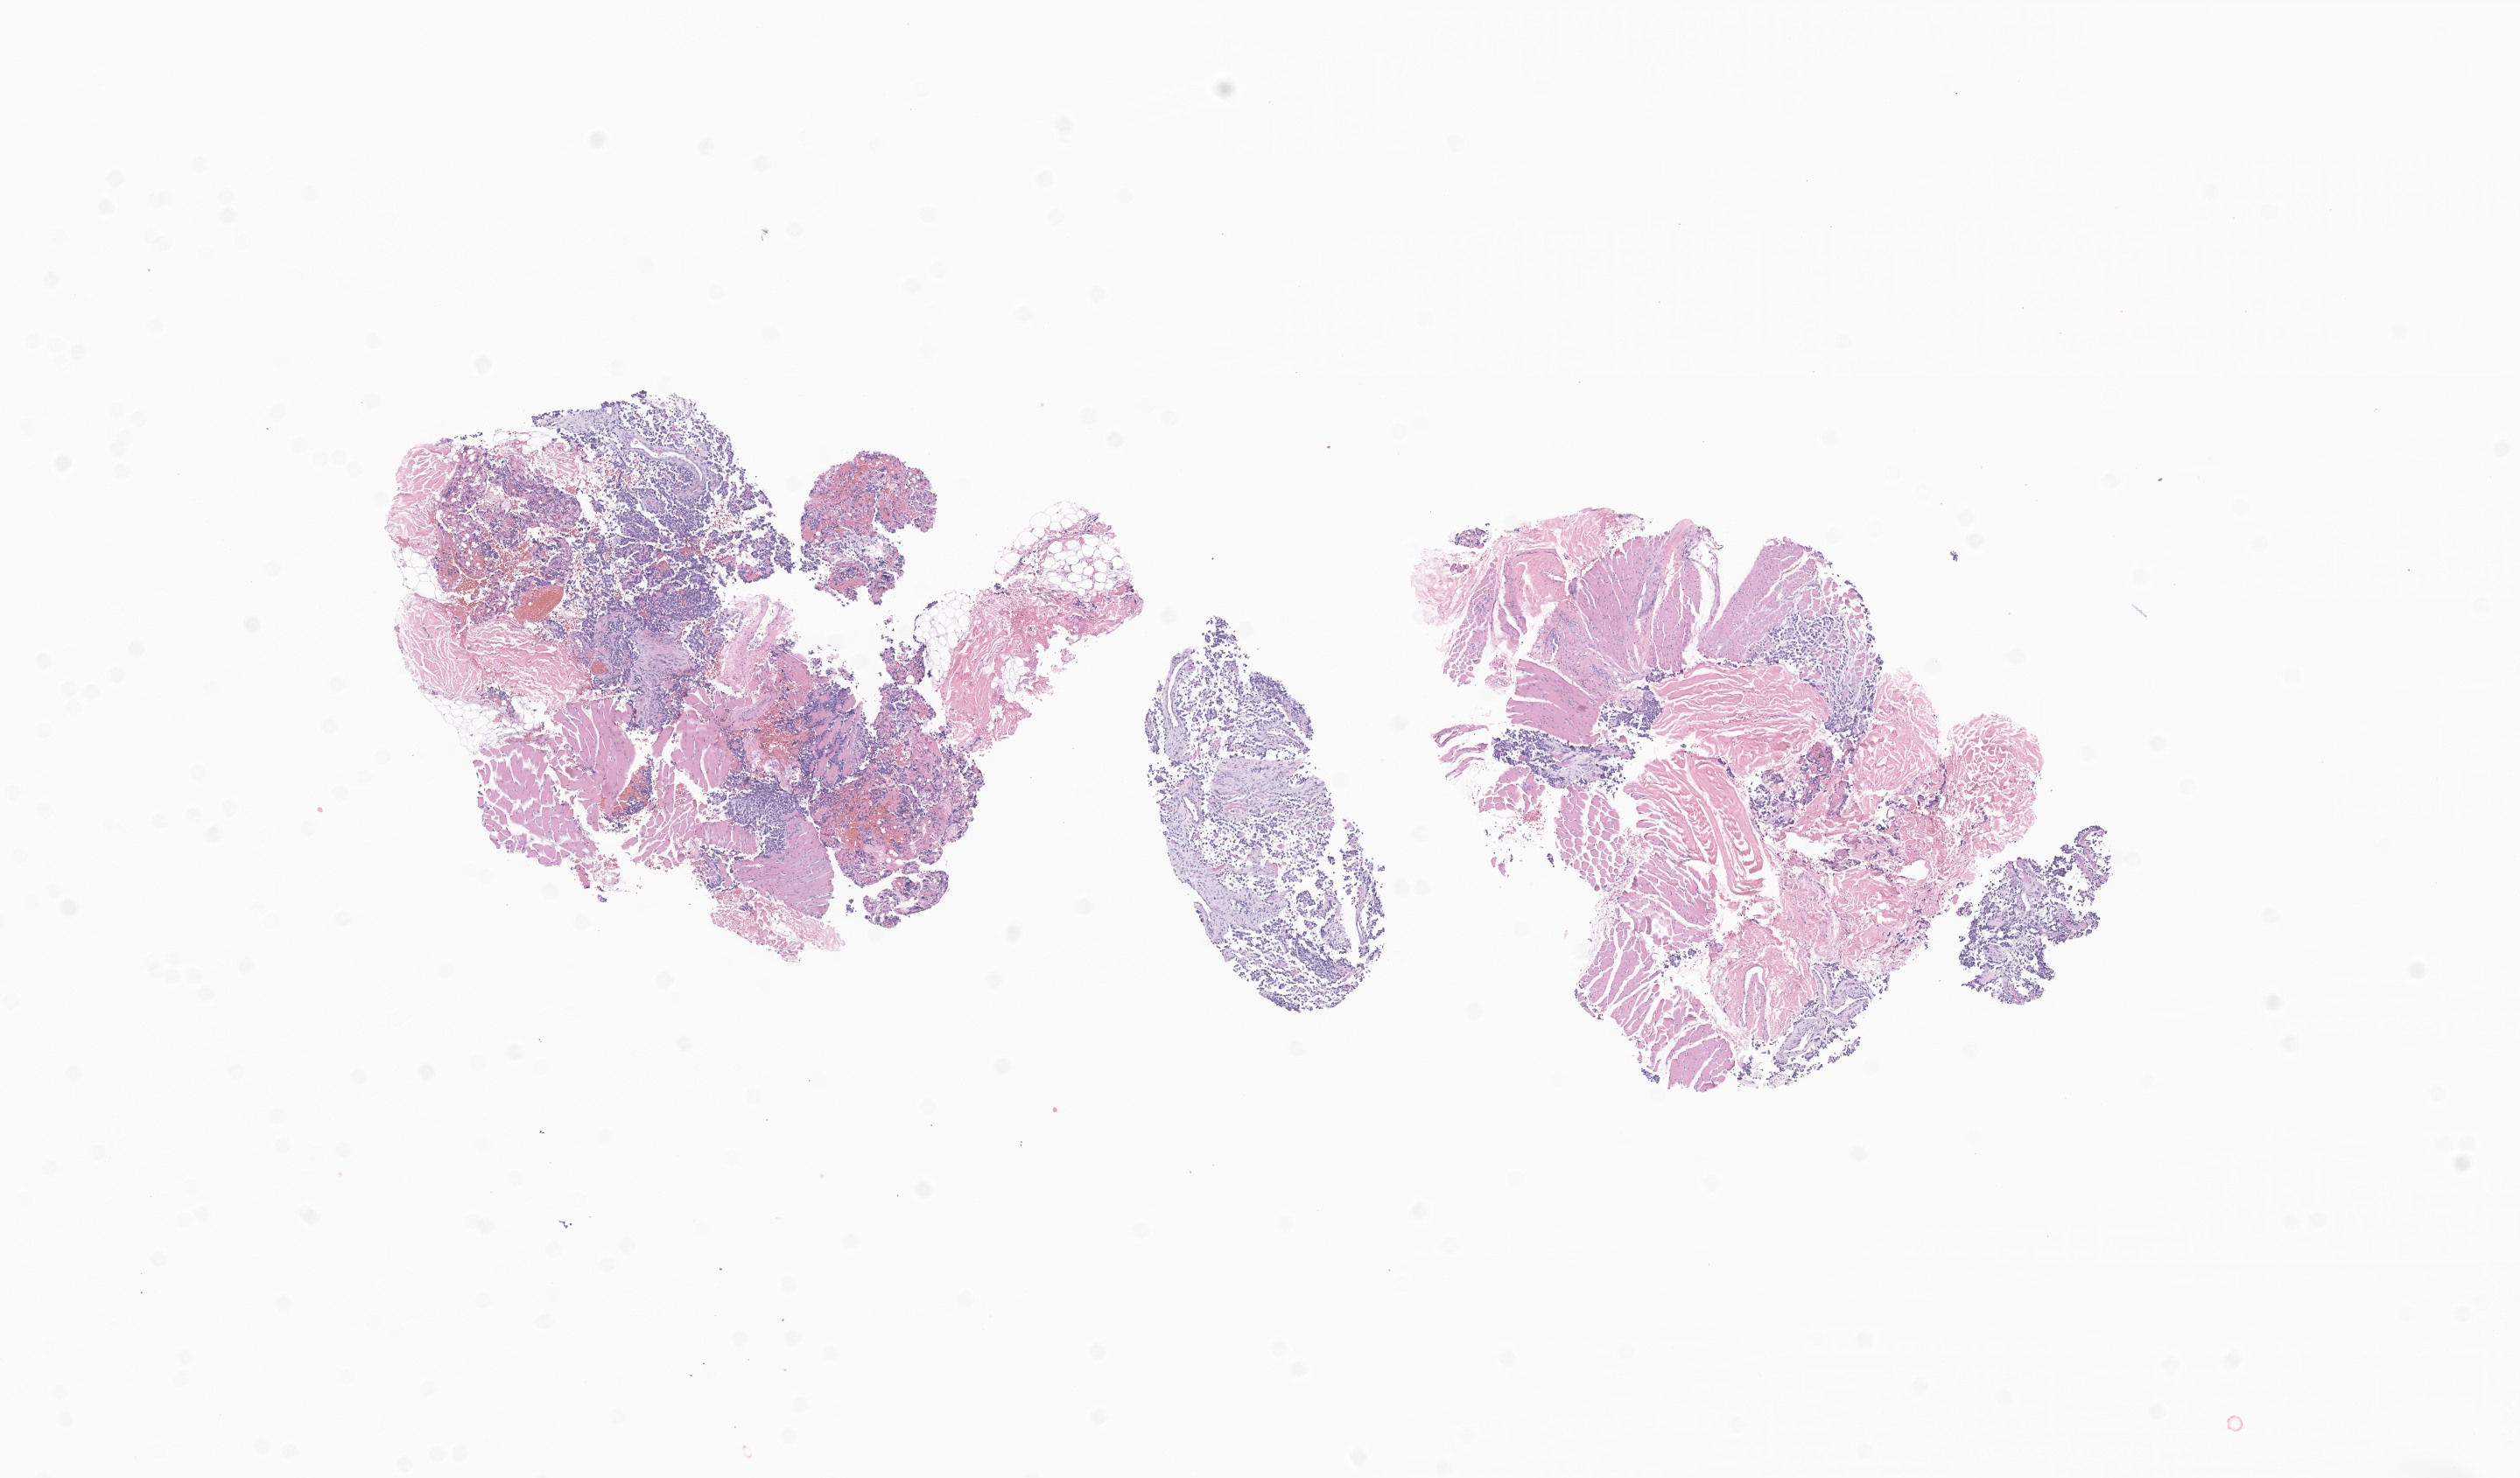
Digitized hematoxylin and eosin (H&E)-stained section of tumor tissue from the head and neck, whole scanned area (about 12.1 x 7.1 mm) shown as a low-resolution overview. Formalin-fixed paraffin-embedded section. Male patient, age 208 months (17 years 4 months).
Diagnosis: Alveolar rhabdomyosarcoma.